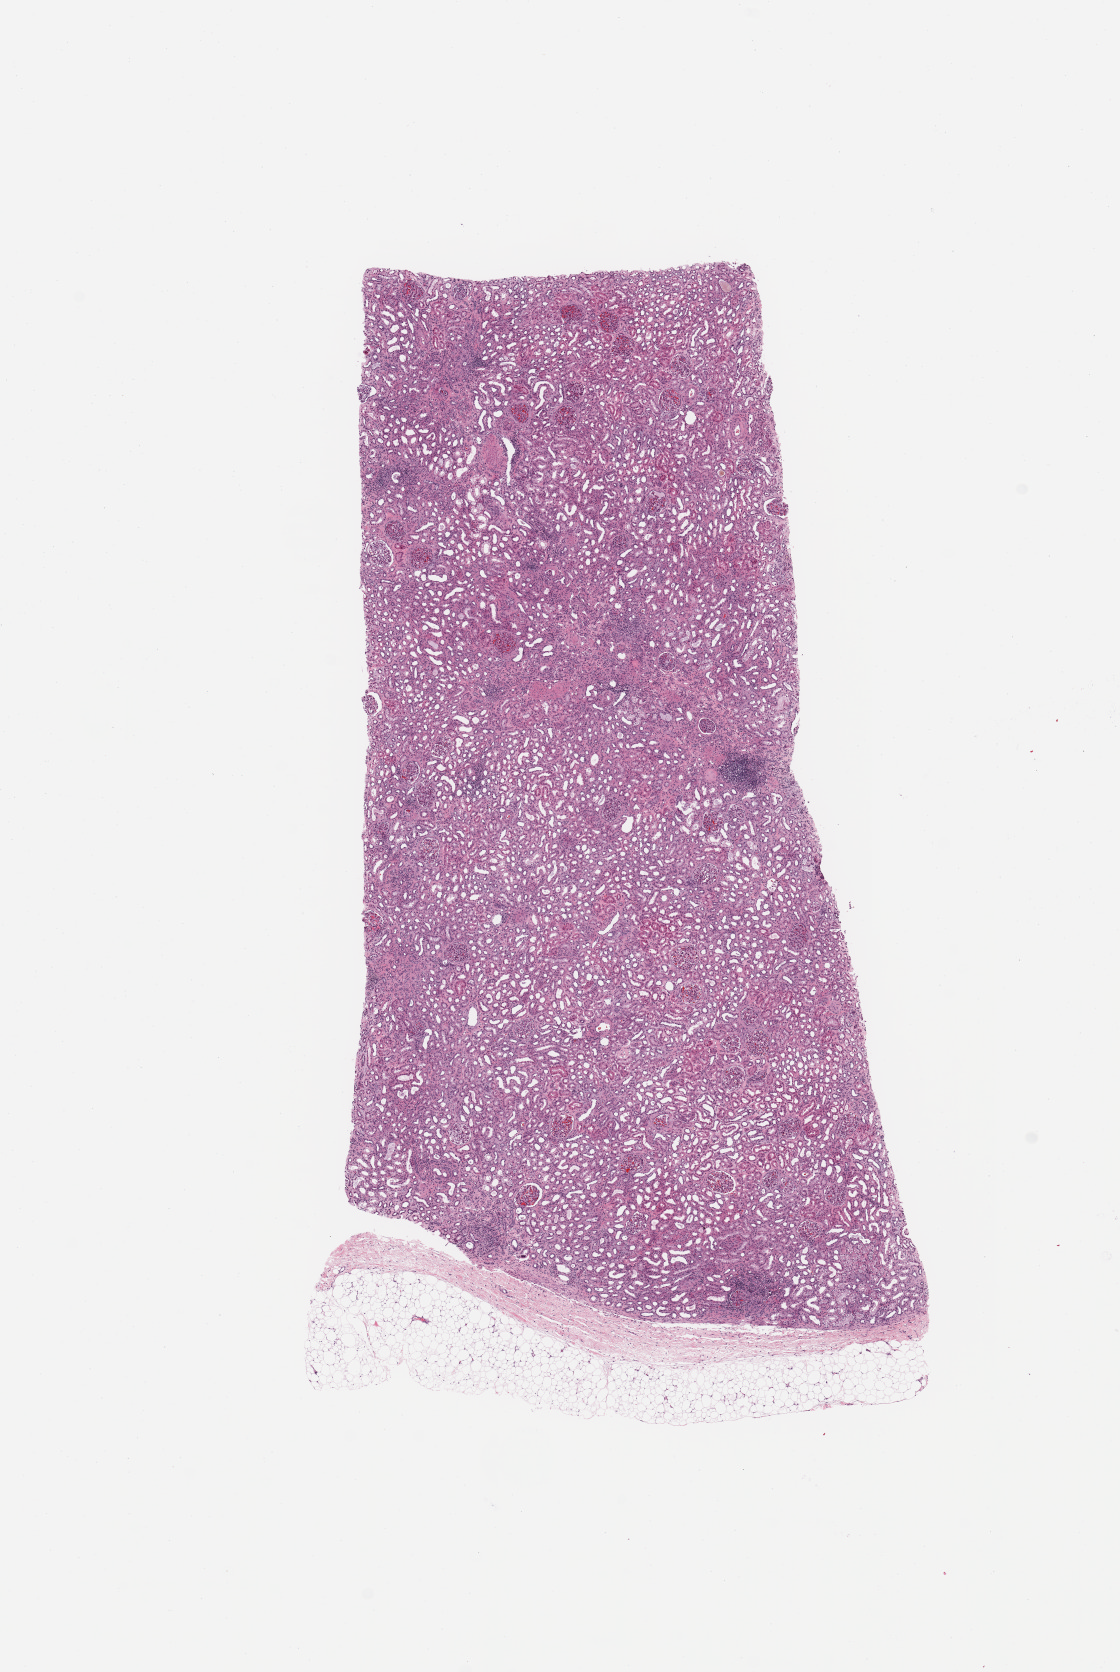
Digitized H&E tissue section (whole slide) — shown as a low-resolution overview of the whole scanned area (about 8.9 x 13.2 mm, slide scanned at 20x); normal (non-tumour) tissue sample, sampled site: kidney. Male, 49 y/o.
- this section: normal (non-tumour) tissue from the same patient
- patient diagnosis: Renal cell carcinoma, NOS